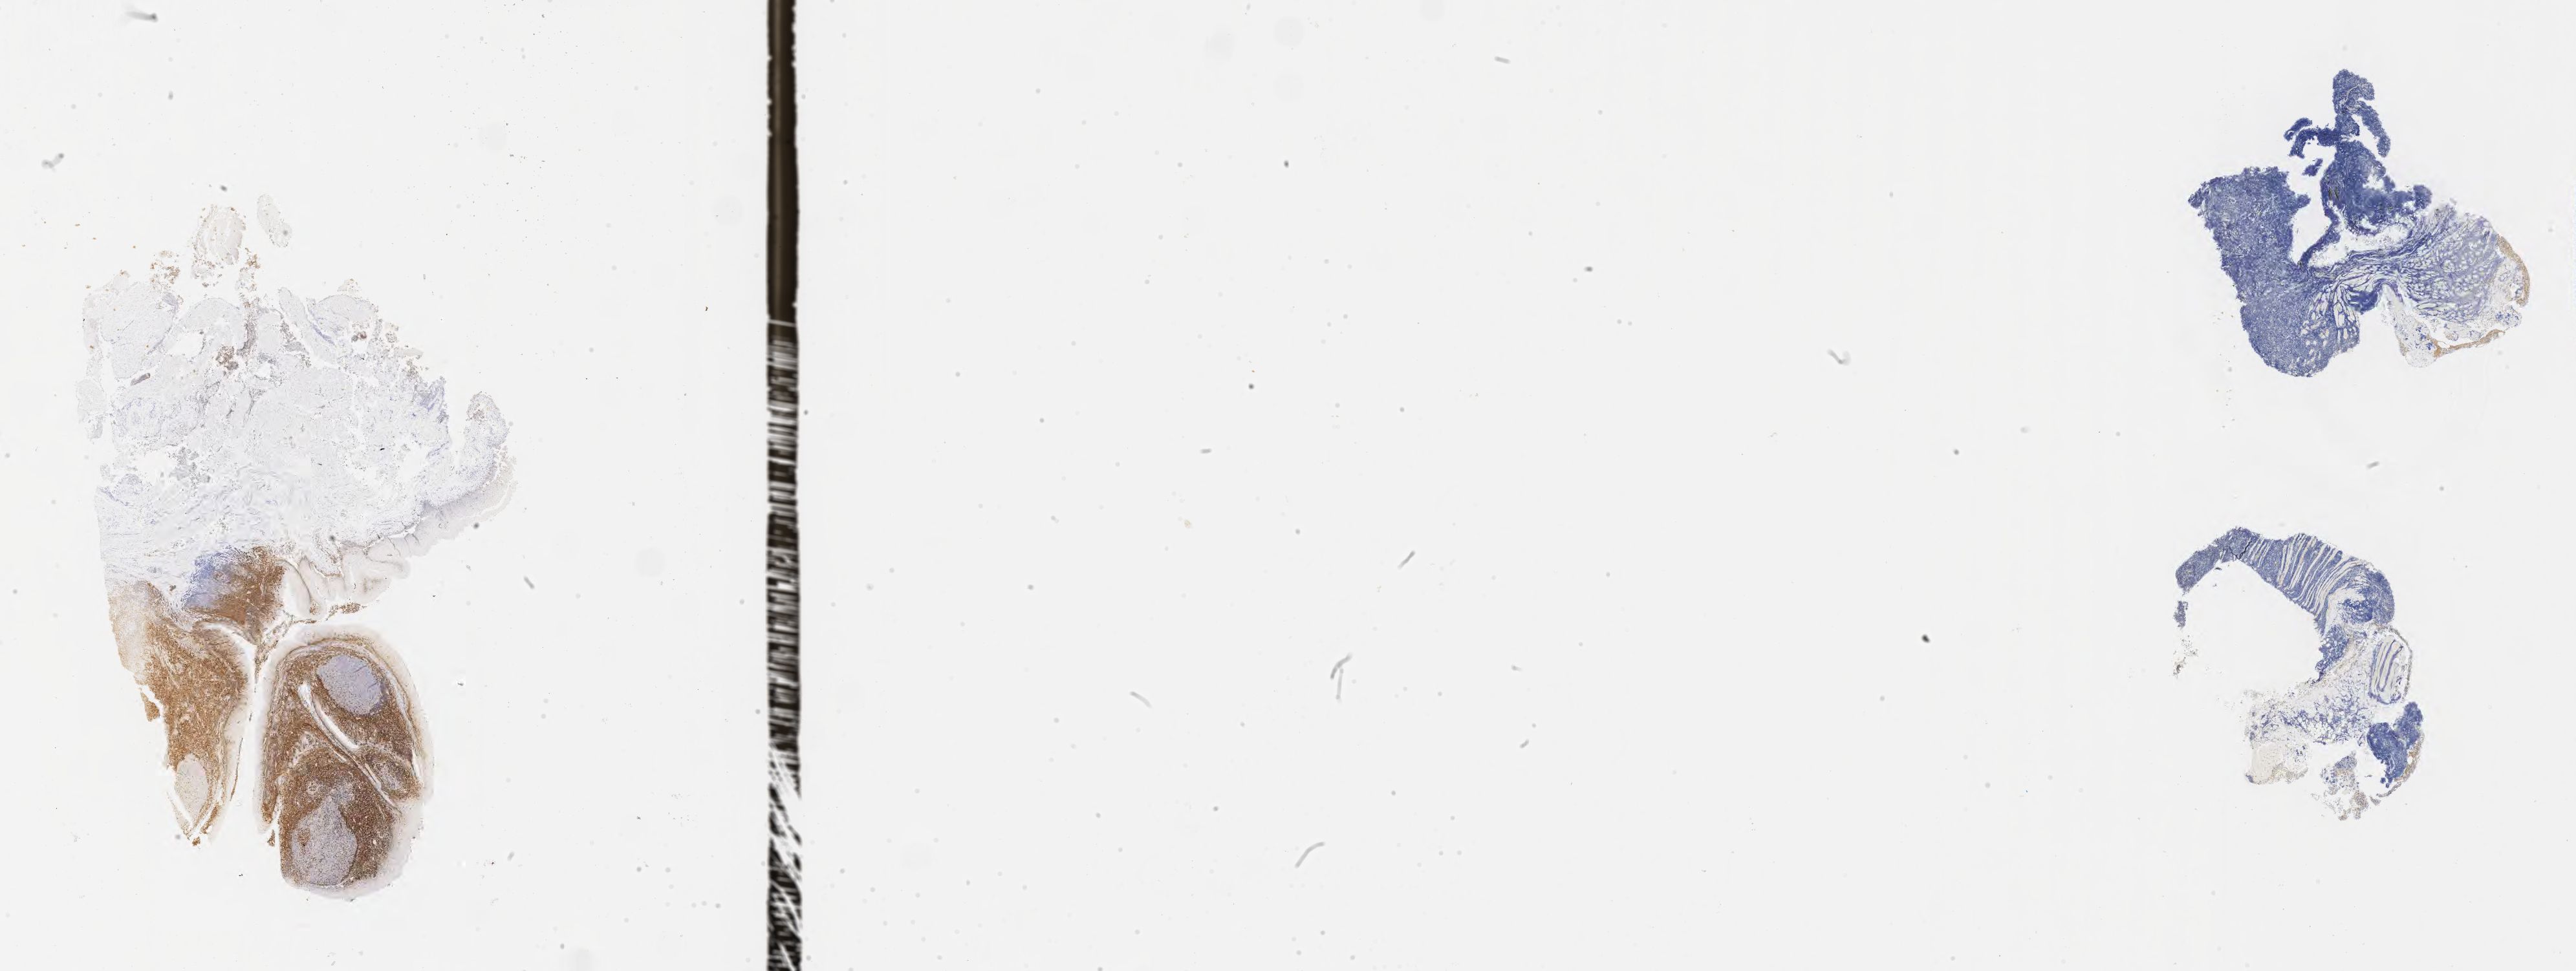
Whole-slide image, immunohistochemical stain for BCL2 — a low-resolution overview of the entire scanned area, about 32.2 x 12.1 mm; tumor tissue; site: lymph node of head and neck. Patient male; aged 73.
Diagnosis: Burkitt lymphoma, NOS.